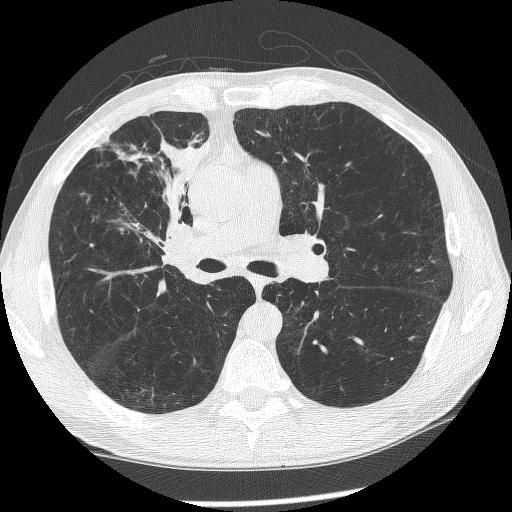
Chest CT (low-dose screening protocol), one axial image. First (baseline) screen. Lung window (W 1500 / L -600 HU). 1.25 mm slice thickness. Slice 144 of 266 in the series. Male participant, aged 60 years at enrolment. Current smoker at enrolment.
Lesion marked by an expert reader, bounding box [x1, y1, x2, y2] px = [145, 189, 219, 282]. Screening reader's record for this exam (one nodule recorded; not confirmed to be the boxed lesion): non-calcified nodule or mass ≥4 mm, right upper lobe, 12 × 8 mm, spiculated (stellate) margins, mixed attenuation. Lung cancer was diagnosed 208 days after this screen: squamous cell carcinoma, NOS, right upper lobe, right middle lobe, right main stem bronchus, poorly differentiated (G3), stage IV (AJCC 6th edition).